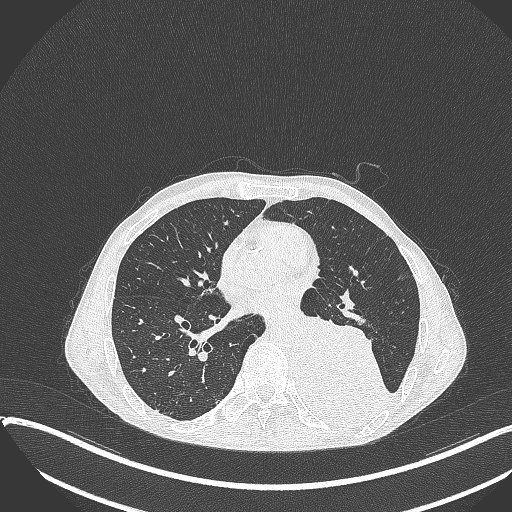
Chest CT, one axial slice; 120 kVp; lung window (W 1500 / L -600 HU); 1 mm slice thickness; 512 × 512 image matrix. Male patient, age 57 years. From the clinical record (not read from this slice): clinical TNM (as recorded): T4 N0 M0.
Annotated regions visible in this slice (rectangle marked by the reading radiologist):
- lung tumour (recorded histology: squamous cell carcinoma): bounding box [x1, y1, x2, y2] px = [294, 310, 394, 434]